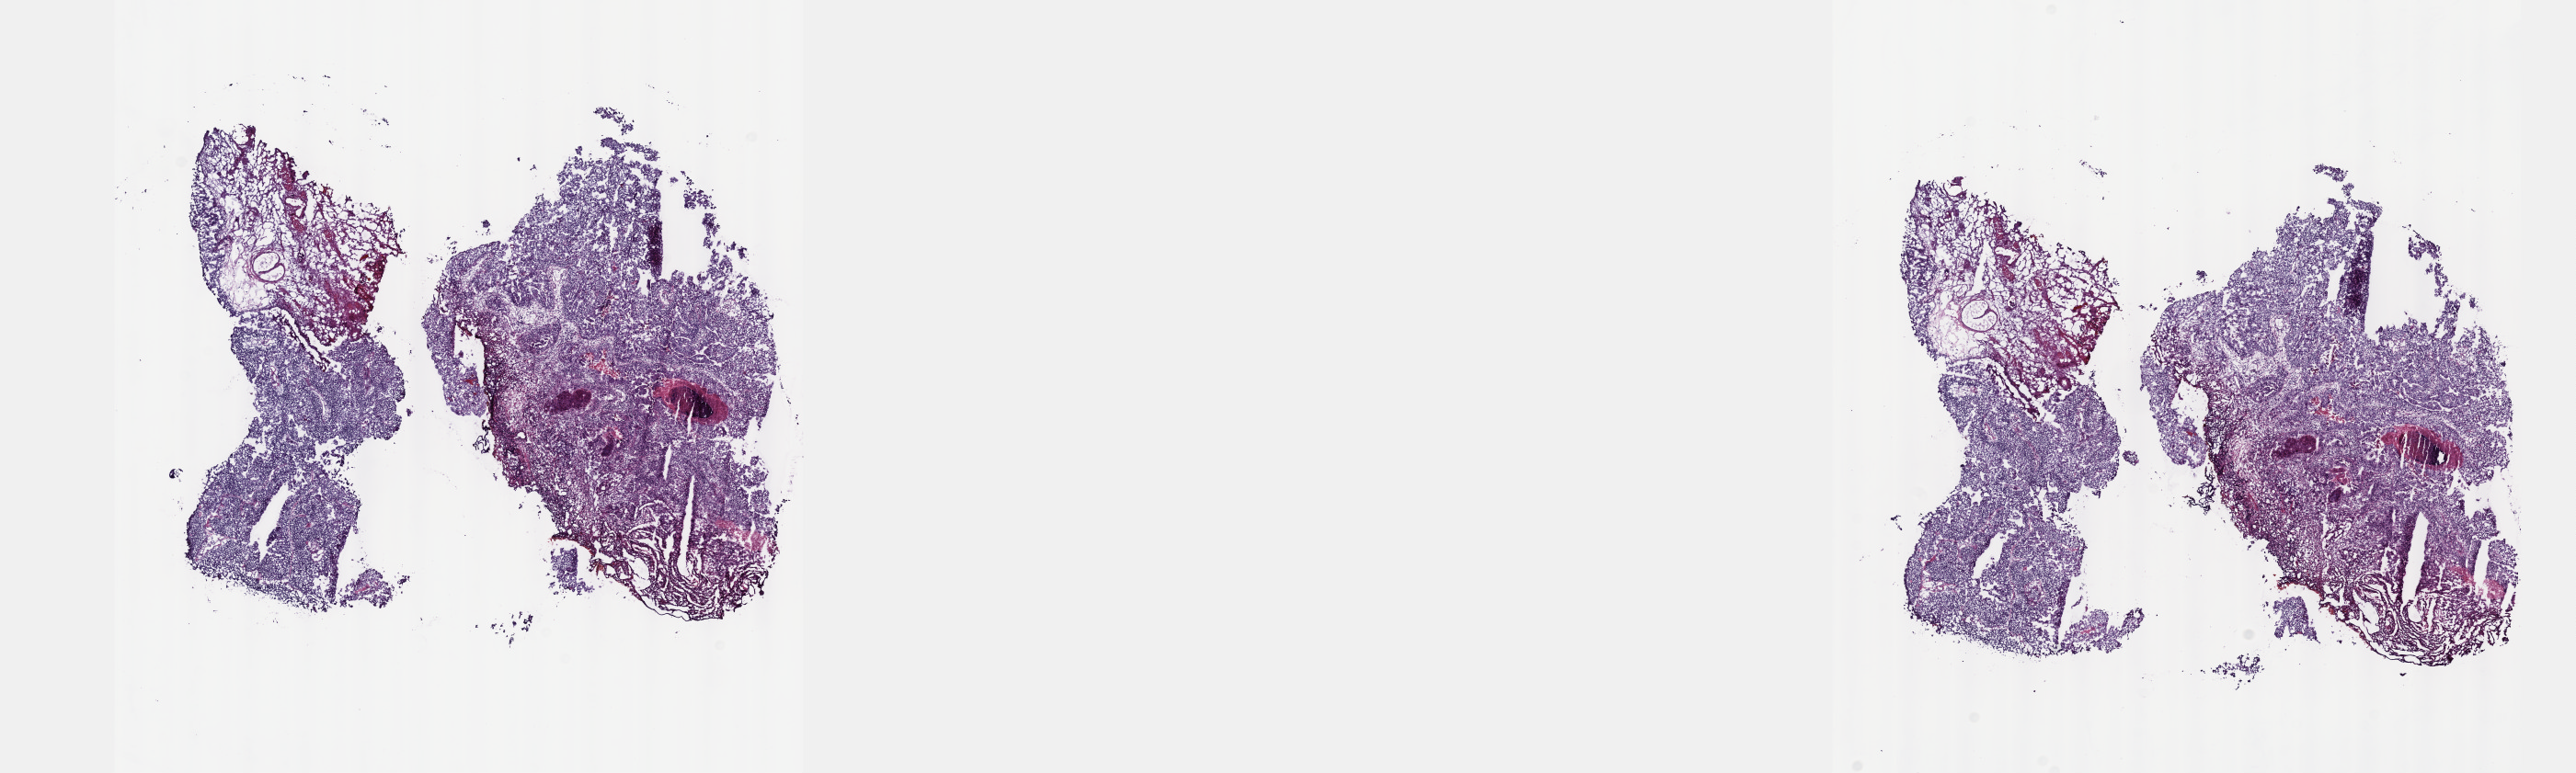
Hematoxylin and eosin (H&E) stained whole-slide image — whole scanned area (about 22.6 x 6.8 mm) shown as a low-resolution overview. Frozen section from the top of the tissue portion. Primary tumour sample from the bladder. Male, age 56 years at initial diagnosis. Histologic grade: high grade. Pathologist review of this section (percent, as recorded): tumour cells 70%, tumour nuclei 90%, normal cells 0%, stromal cells 10%, necrosis 20%. Infiltration values recorded for this section: lymphocyte infiltration 0%, monocyte infiltration 0%, neutrophil infiltration 0%.
* TNM: T2 NX M0
* AJCC pathologic stage: II (6th edition)
* diagnosis: Transitional cell carcinoma